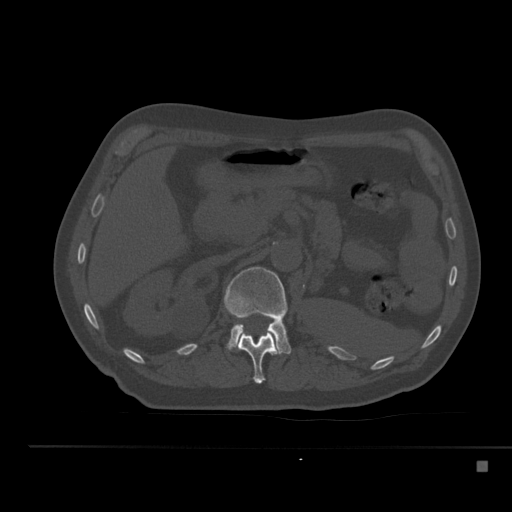
CT including the spine, one axial slice; slice 218 of 517 in the series (ordered by position); reconstruction kernel Br40s; 120 kVp; bone window (W 1800 / L 400 HU); 512 × 512 image matrix. Patient: male, 70 years. From the clinical record (not read from this slice): primary cancer: renal; vertebrae with lytic lesions (as recorded): T4, T6, T10, T12, L3, L4, L5.
Structures marked on this image (semi-automatically segmented with operator editing):
- L1 vertebra: box from (x=224, y=267) to (x=291, y=354) px
- T12 vertebra: (x=236, y=331)–(x=278, y=384)